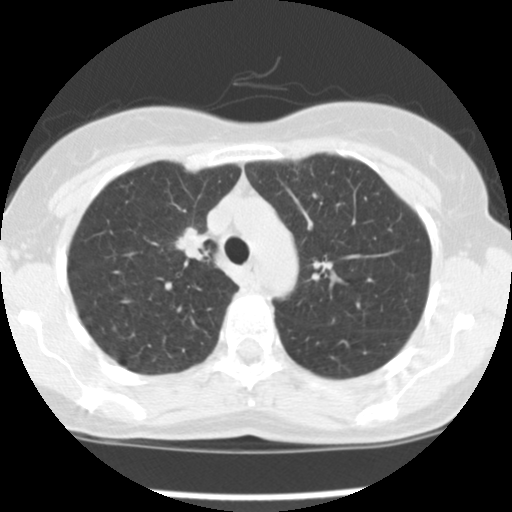
Low-dose screening chest CT, axial slice. Baseline screening round. Lung window (W 1500 / L -600 HU). 2.5 mm slice thickness. Slice 115 of 157 in the series. 512 × 512 image matrix. Female, age 57 years at enrolment. Current smoker at enrolment.
• Lesion marked by an expert reader, bounding box (x1, y1, x2, y2) in pixels: (166, 227, 217, 271).
• Reader record for this screening exam (exam-level; its link to the box is not recorded): non-calcified nodule or mass ≥4 mm, left upper lobe, 7 × 6 mm, poorly defined margins, ground glass attenuation.
• Note: the box lies in the patient's right hemithorax on this image, whereas the reader's record names the left lung; they may be different findings.
• Official screen result: positive, change unspecified: nodule(s) >= 4 mm or enlarging nodule(s), mass(es), or other non-specific abnormalities suspicious for lung cancer.
• Participant outcome: lung cancer diagnosed 15 days after this screen — adenocarcinoma, NOS, right upper lobe, moderately differentiated (G2), stage IA (AJCC 6th edition), 15 mm at pathology.